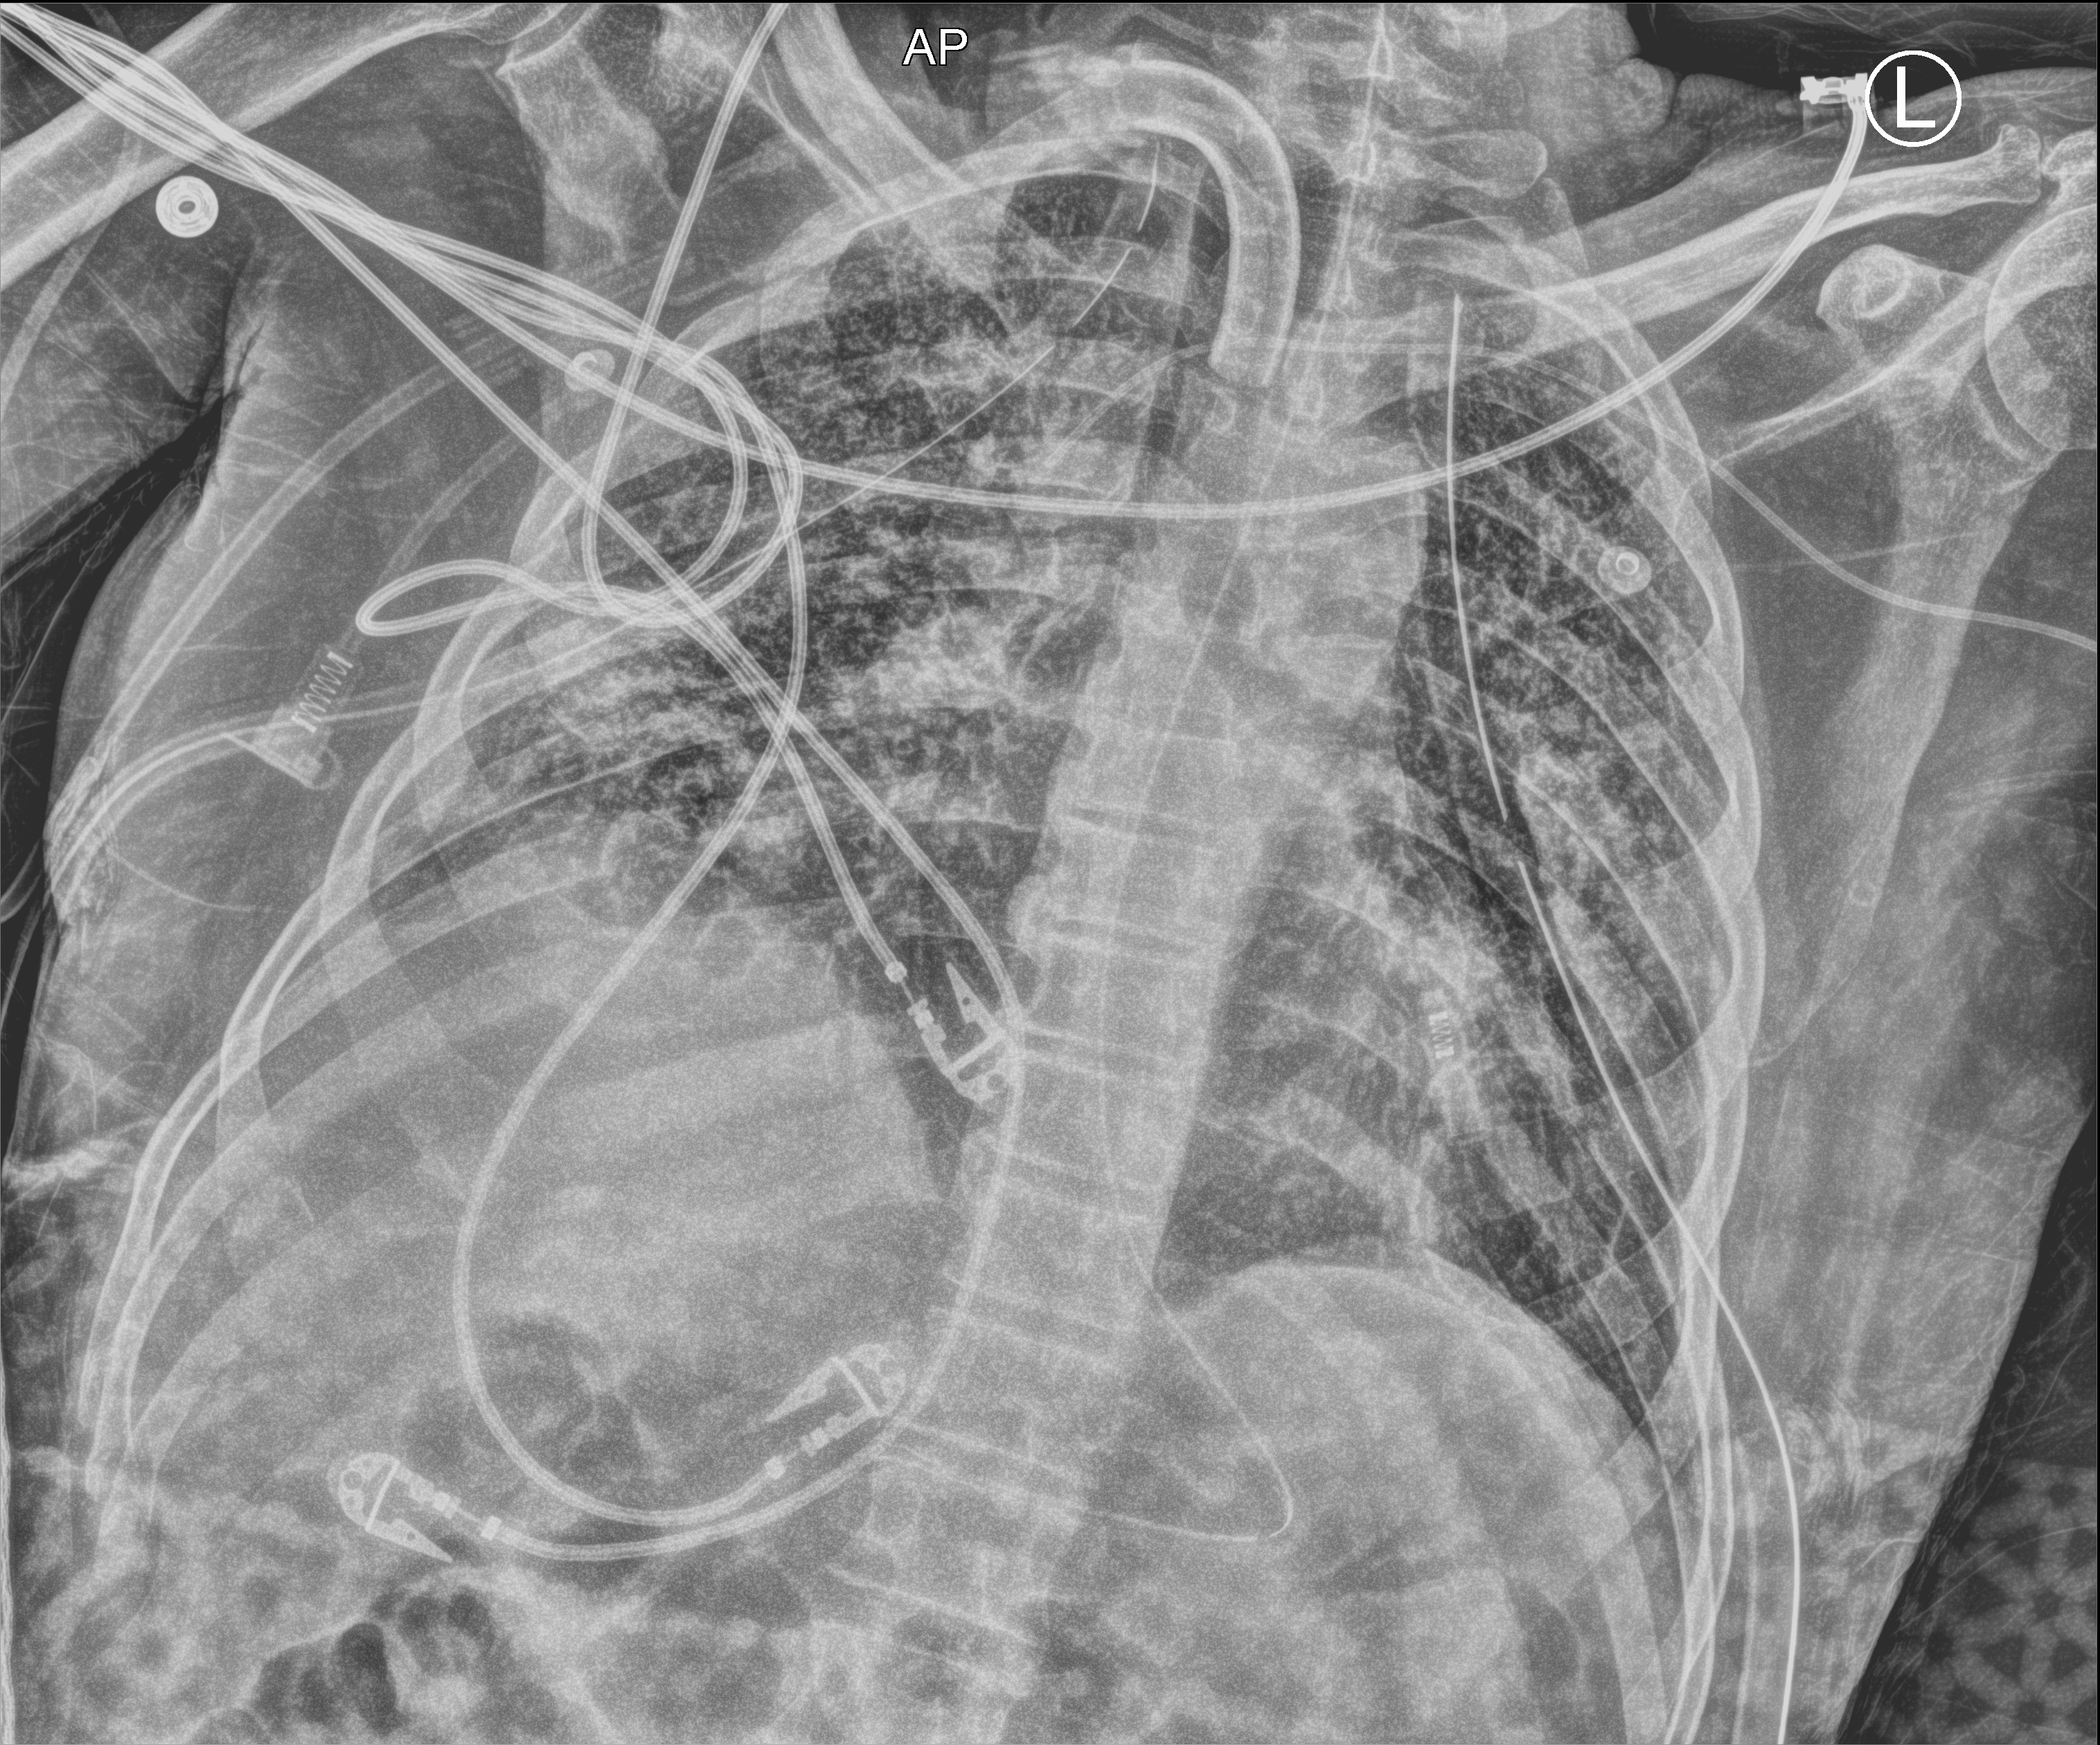
Portable chest radiograph; anteroposterior (AP) projection. Male patient hospitalised with COVID-19, age 18–59 years.
Hospital-stay facts (about this admission, not read from this image; timing relative to this image not recorded): admitted to intensive care during this hospital stay: yes; length of hospital stay: 83 days; mechanically ventilated during this hospital stay: yes.